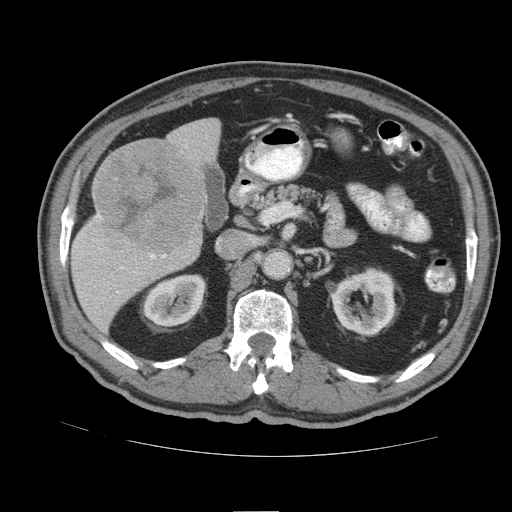
Contrast-enhanced abdominal CT (liver protocol), one axial slice. Slice 44 of 105 in the series (ordered by position). 140 kVp. Soft-tissue window (W 400 / L 40 HU). 512 × 512 image matrix, field of view 380 × 380 mm. Case-level facts recorded for this patient, not image findings: diagnosis: hepatocellular carcinoma (patient treated with transarterial chemoembolisation; whether this scan precedes or follows treatment is not stated here); TNM stage (as recorded): Stage-IIIB; Child-Pugh class: A.
Outlined on this slice (semi-automatically segmented with operator editing):
- liver parenchyma outside the tumour (the mass and vessels are separate outlines, so this box may not span the whole liver): bounding box (x1, y1, x2, y2) in pixels: (70, 118, 220, 332)
- mass: (95, 142, 203, 252)
- liver vessels: (150, 254, 166, 259)